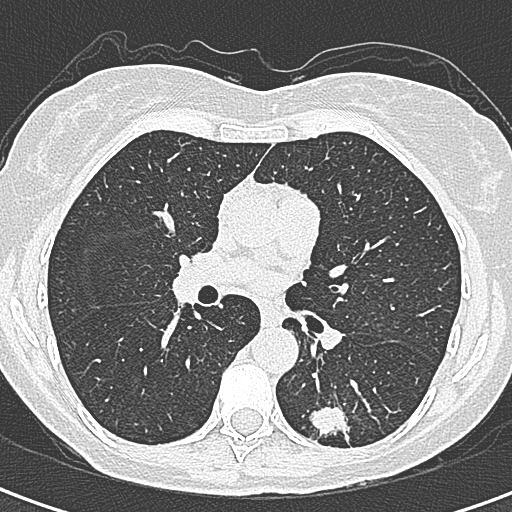
Low-dose screening chest CT, axial slice, baseline annual screen, lung window (W 1500 / L -600 HU), 1 mm slice thickness, lung (sharp) reconstruction kernel (B80f), slice 139 of 328 in the series. Female, age 58 years at enrolment. Former smoker at enrolment.
- Lesion marked by an expert reader, bounding box <298,386,367,456> (left, top, right, bottom; pixels).
- The screening reader recorded 2 non-calcified nodules or masses ≥4 mm on this exam (left lower lobe, right lower lobe); which of them this box marks is not recorded.
- Later outcome: lung cancer diagnosed 22 days after this screen — adenocarcinoma, NOS, left lower lobe, moderately differentiated (G2), stage IA (AJCC 6th edition), 25 mm at pathology.